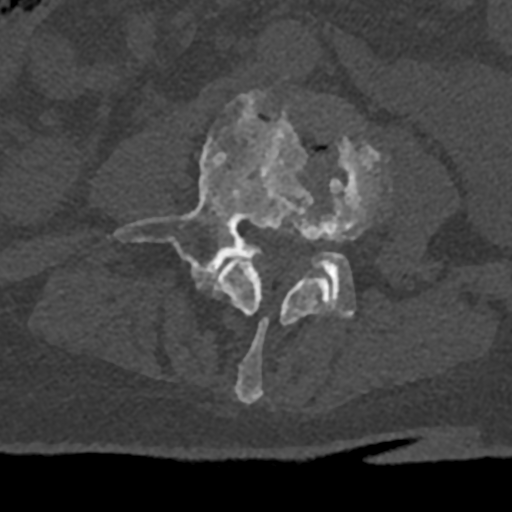
CT including the spine, one axial slice. Position 285 of 797 along the scan axis. Reconstruction kernel Br40s/3. Bone window (W 1800 / L 400 HU). 512 × 512 image matrix. Patient: male, 74 years. Case-level facts recorded for this patient, not image findings: primary cancer: renal; vertebrae with lytic lesions (as recorded): T10, L1, L2, L3, L4, L5.
Outlined on this slice (semi-automatically segmented with operator editing):
- L3 vertebra: bounding box [x1, y1, x2, y2] px = [215, 130, 389, 404]
- L4 vertebra: [107, 91, 354, 318]